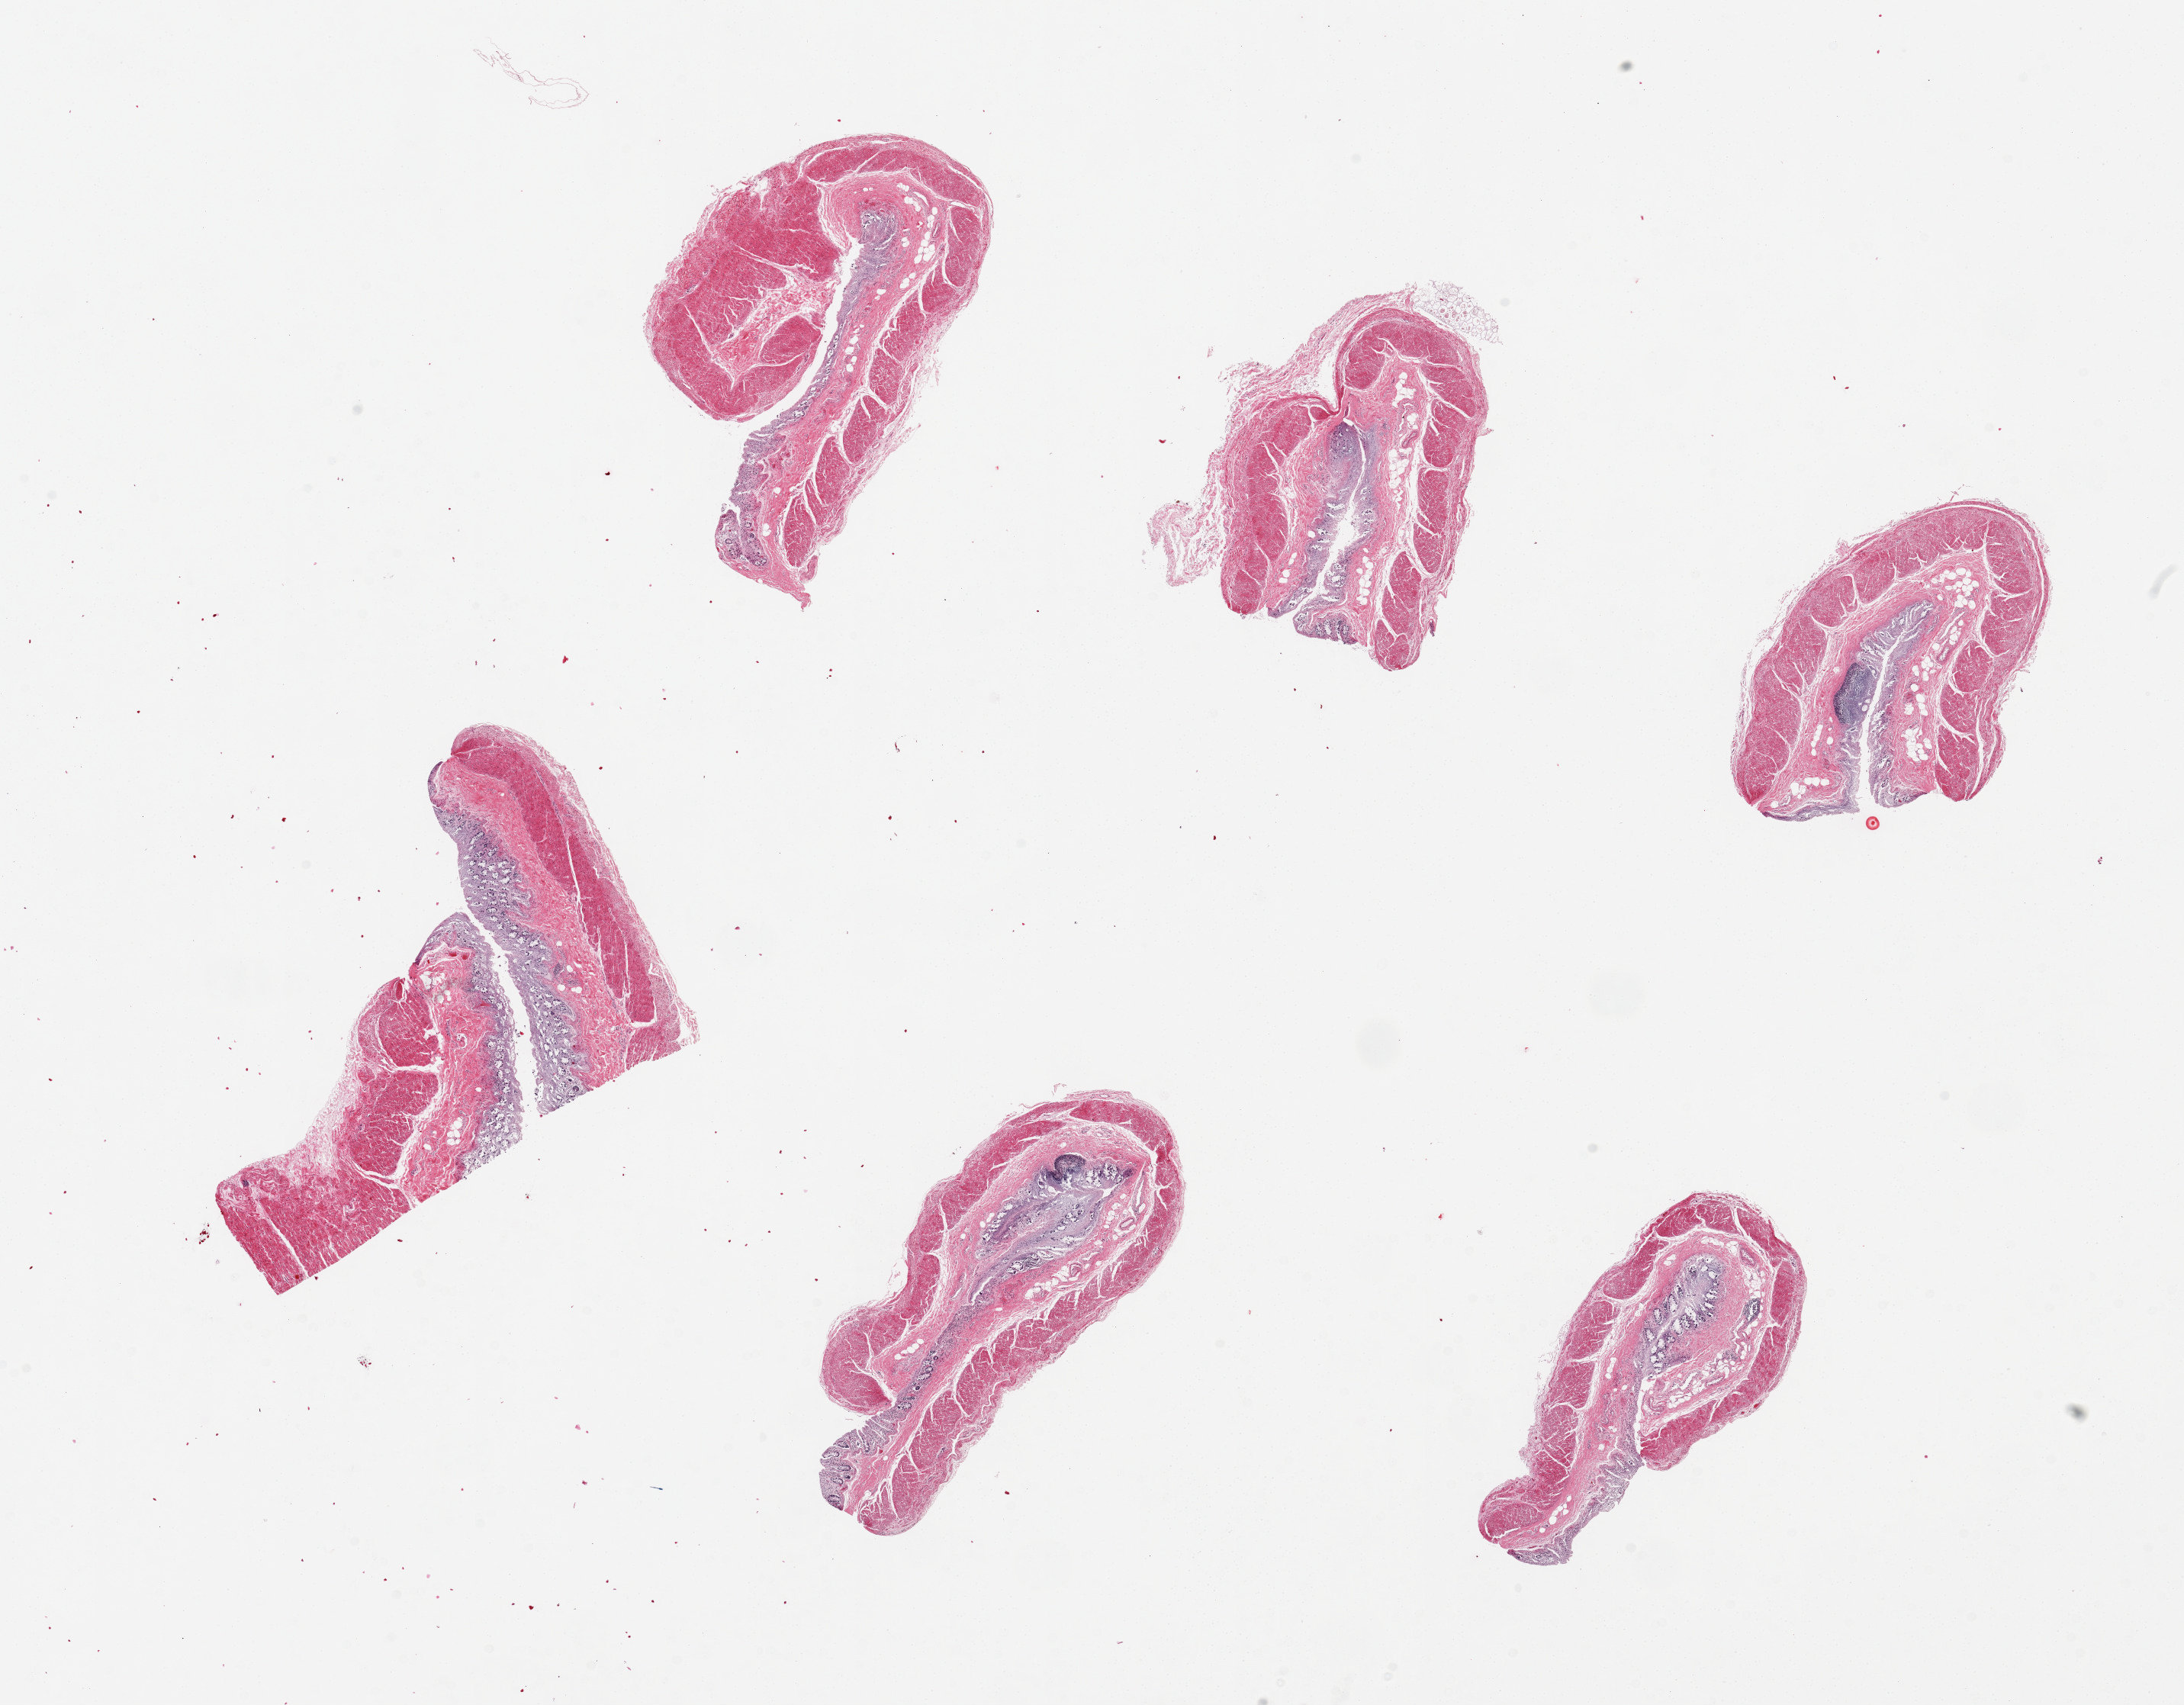
Digitized haematoxylin and eosin-stained section — a low-resolution overview of the entire scanned area, about 22.6 x 17.7 mm (acquisition: 20x scan); PAXgene-fixed, paraffin-embedded tissue; section of transverse colon (target tissue); tissue donor sample. Female donor.
* reviewer comment on this tissue sample: 6 pieces, mucosa up to ~0.5mm thick but badly preserved and partly sloughed